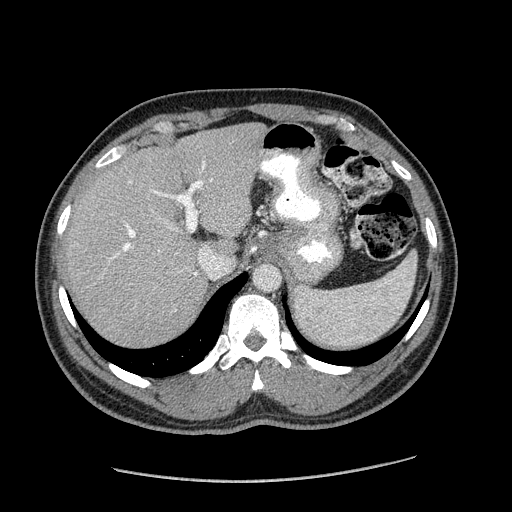
Contrast-enhanced abdominal CT (liver protocol), one axial slice. Reconstruction kernel STANDARD. Soft-tissue window (W 400 / L 40 HU). 2.5 mm slice thickness. 512 × 512 image matrix, field of view 400 × 400 mm. Case-level facts recorded for this patient, not image findings: diagnosis: hepatocellular carcinoma (patient treated with transarterial chemoembolisation; whether this scan precedes or follows treatment is not stated here); TNM stage (as recorded): Stage-I; Child-Pugh class: A; tumour nodularity: uninodular.
Outlined on this slice (semi-automatically segmented with operator editing):
- liver parenchyma outside the tumour (the mass and vessels are separate outlines, so this box may not span the whole liver): bounding box (x1, y1, x2, y2) in pixels: (62, 122, 266, 345)
- liver vessels: (111, 162, 212, 276)